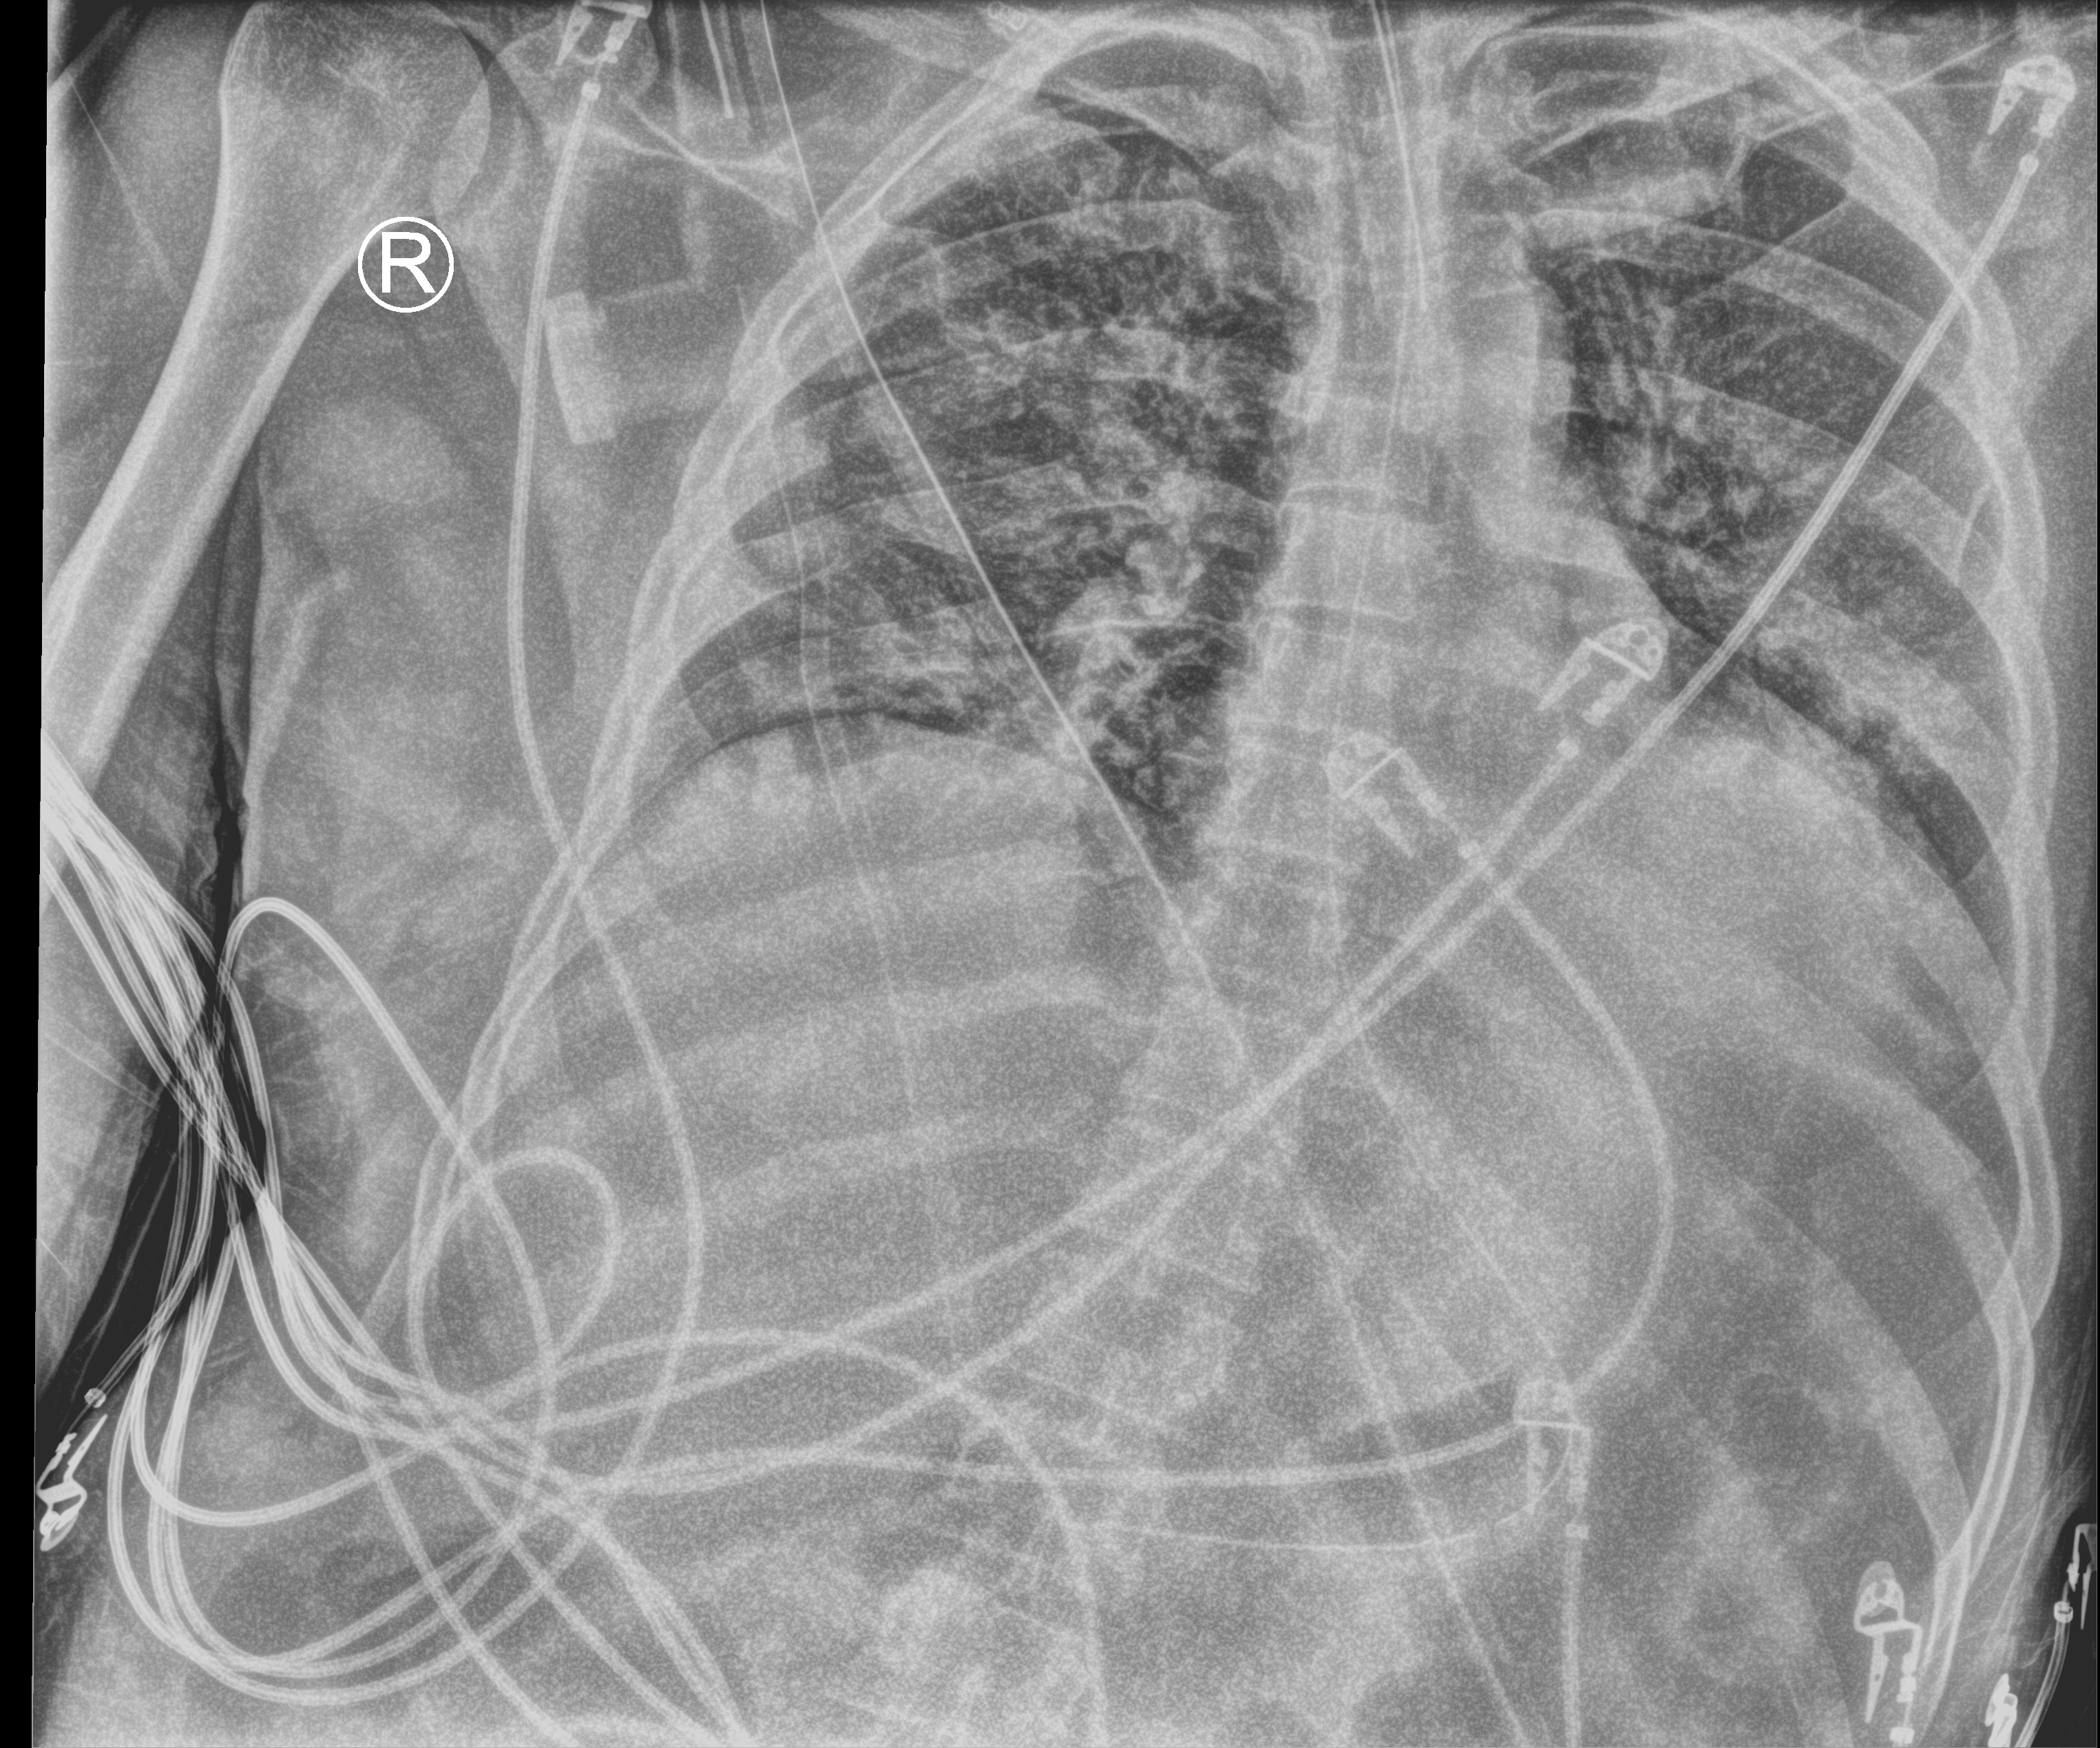
Portable chest radiograph, anteroposterior (AP) projection. Male patient hospitalised with COVID-19, age 18–59 years.
Hospital-stay facts (about this admission, not read from this image; timing relative to this image not recorded): mechanically ventilated during this hospital stay: yes.